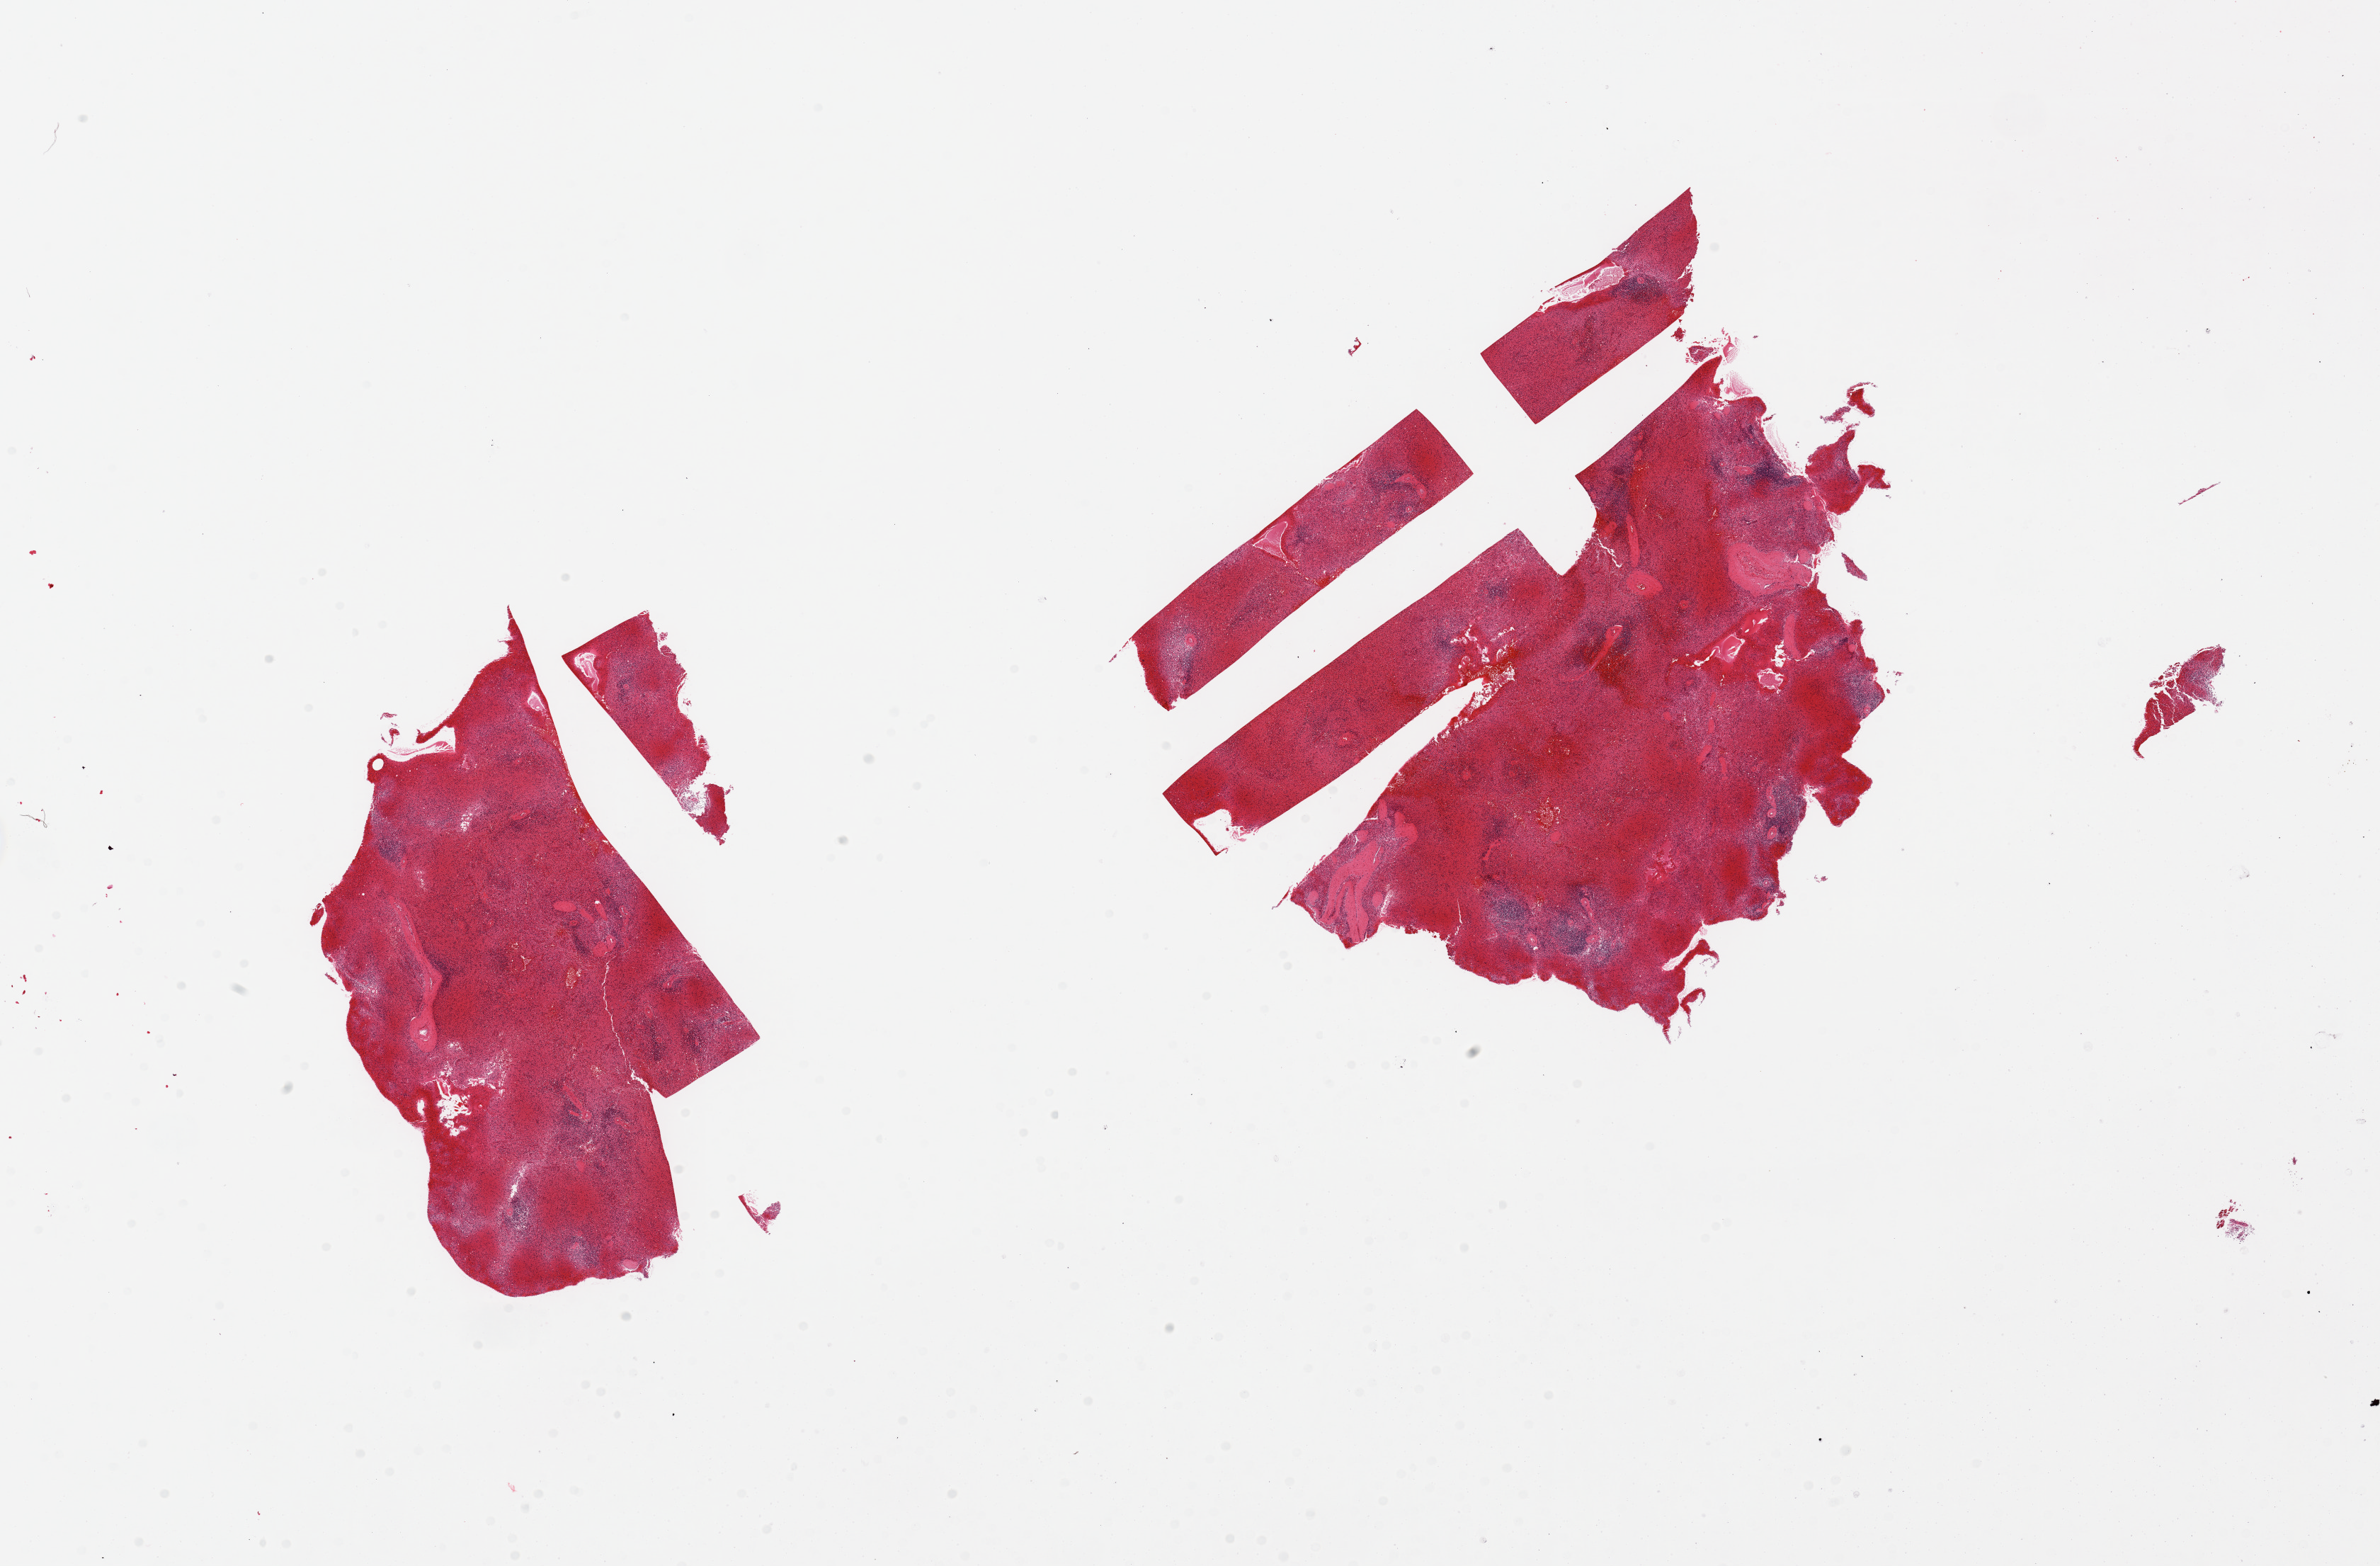
Whole-slide image, haematoxylin and eosin stain — shown as a low-resolution overview of the whole scanned area (about 26.6 x 17.5 mm, acquisition: 20x scan), PAXgene-fixed paraffin-embedded (PFPE) section, target tissue: spleen, donor tissue sample. Donor sex: male.
Review note (as recorded): 2 pieces. Red pulp very congested.